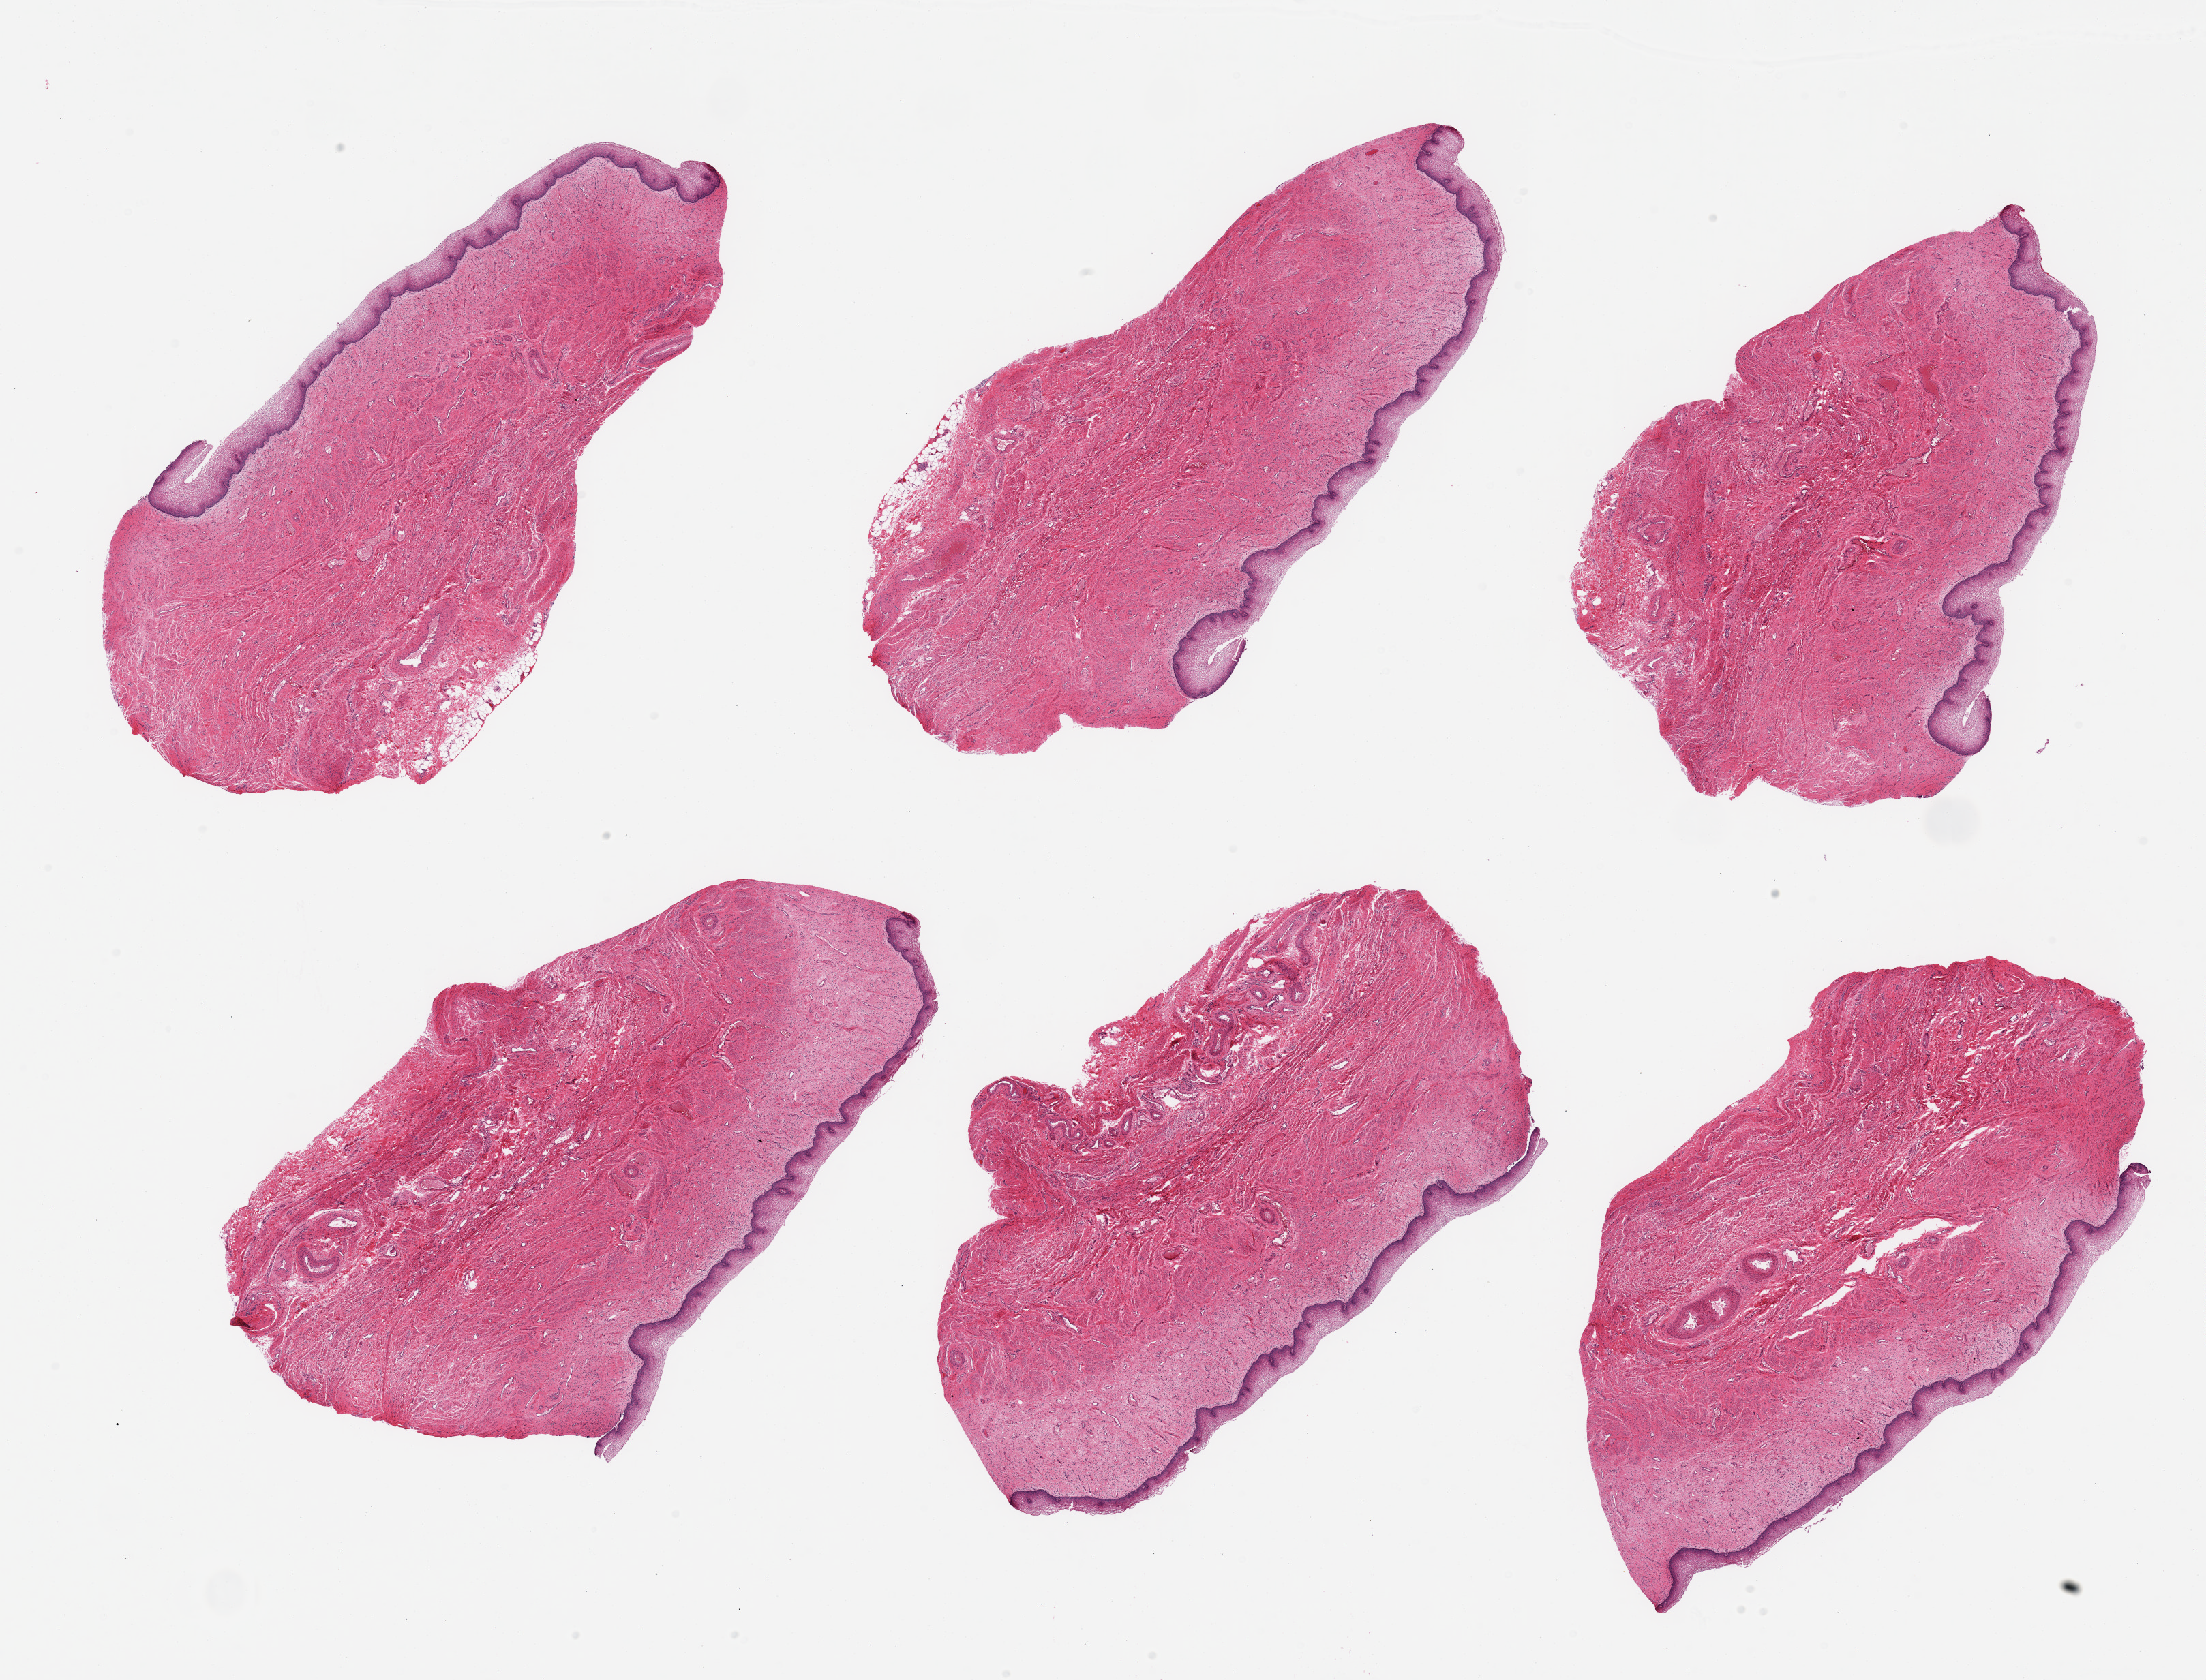
Hematoxylin and eosin (H&E) whole-slide image, whole scanned area (about 25.6 x 19.5 mm) shown as a low-resolution overview. PAXgene-fixed, paraffin-embedded tissue. Target tissue: vagina. Donor tissue sample. Donor sex: female.
Reviewer comment on this tissue sample: 6 pieces; all full thickness with no lesions in epithelium.